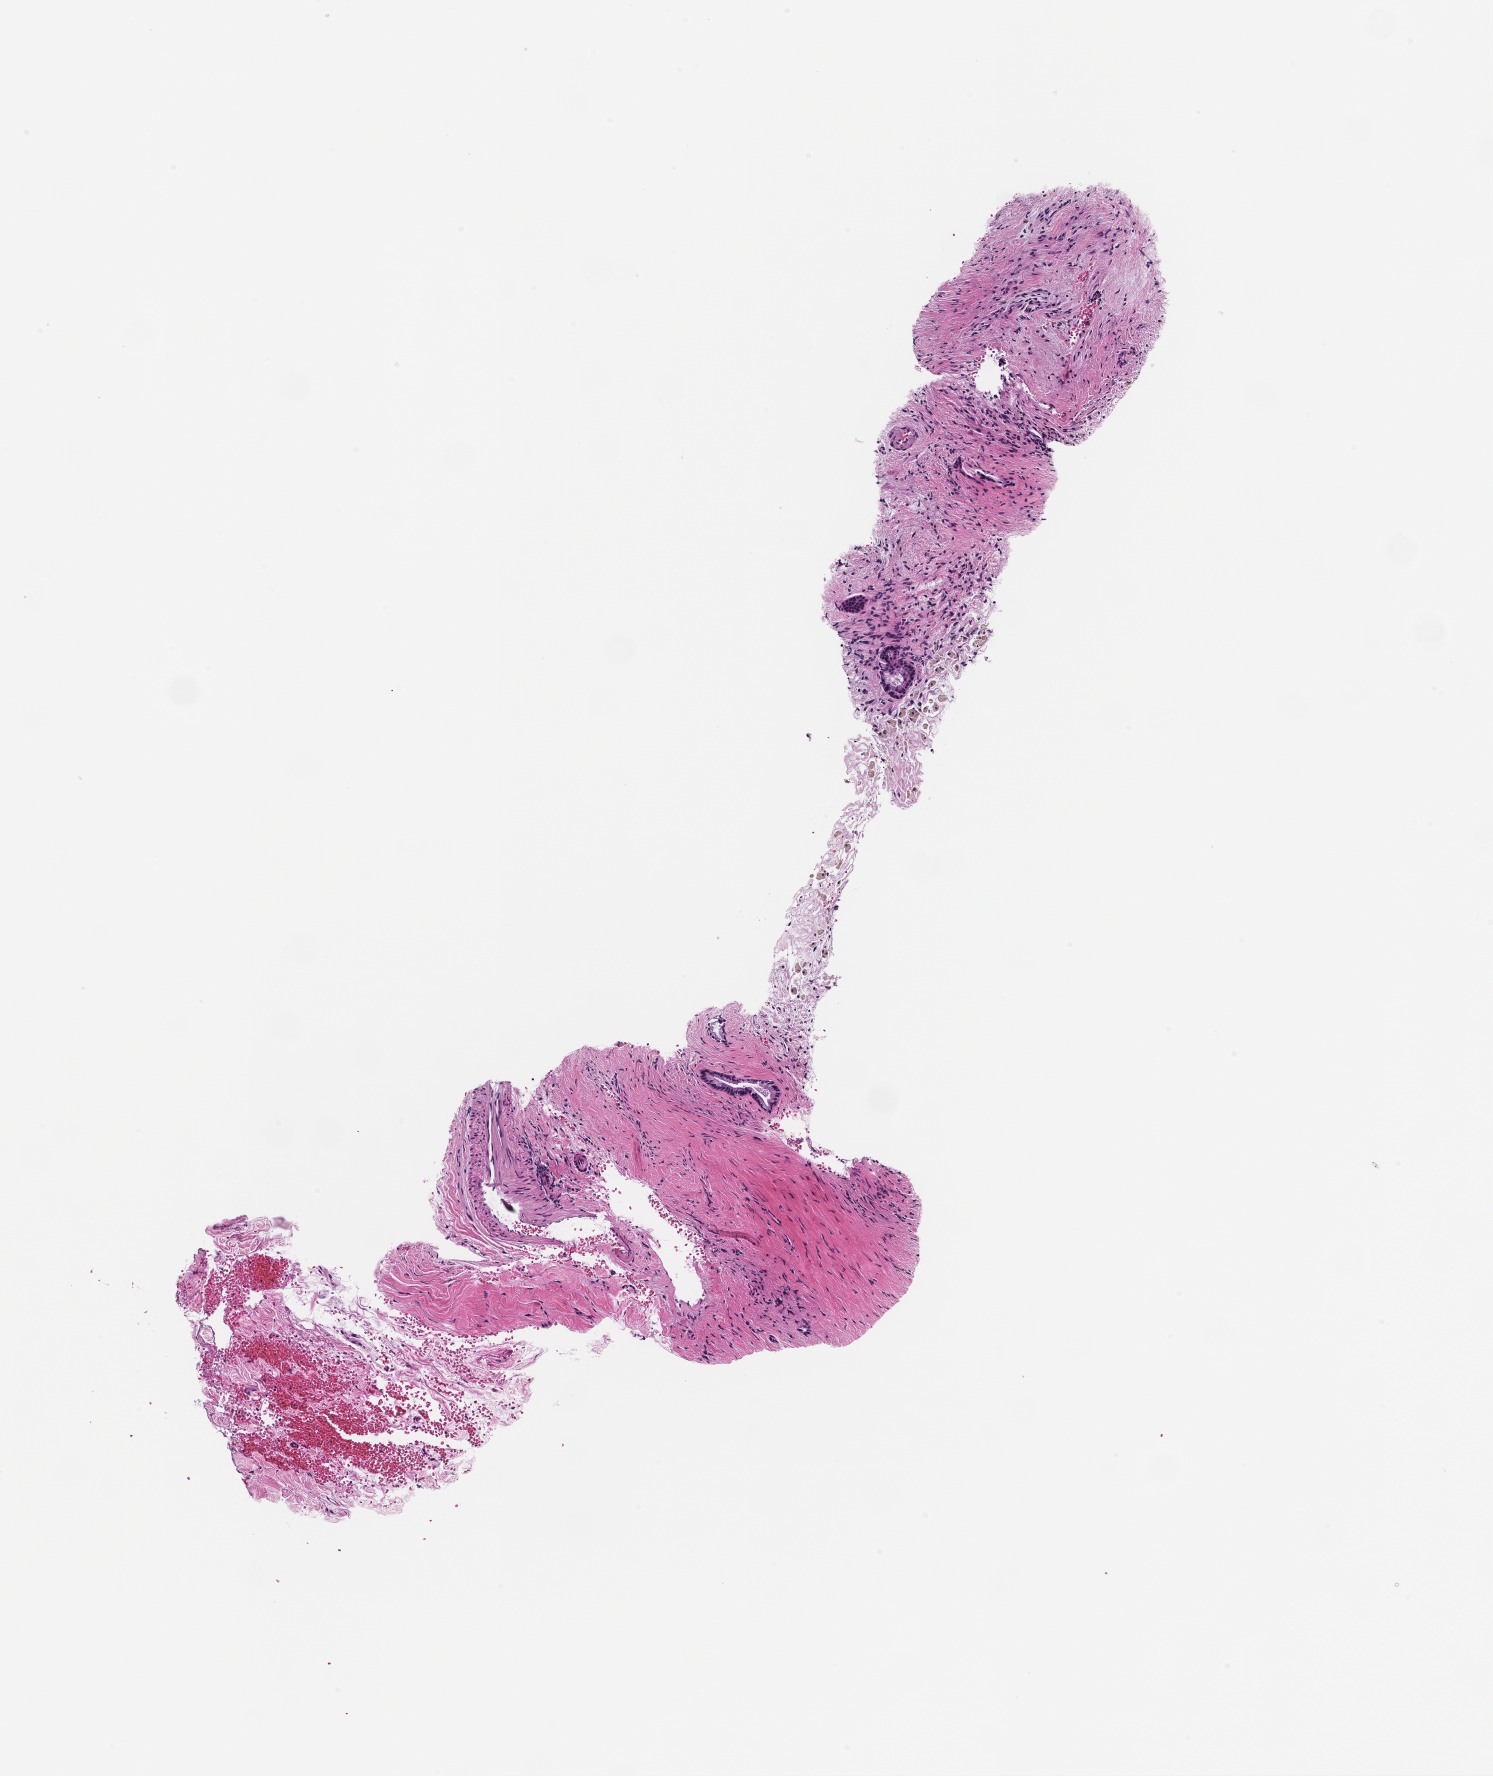
Whole-slide image, haematoxylin and eosin stain — a low-resolution overview of the entire scanned area, about 3.0 x 3.6 mm. FFPE section. Specimen time point: collected at disease progression. Patient sex: female.
This section: metastasis (sampled organ not recorded). Primary diagnosis of the patient: Invasive Breast Carcinoma.